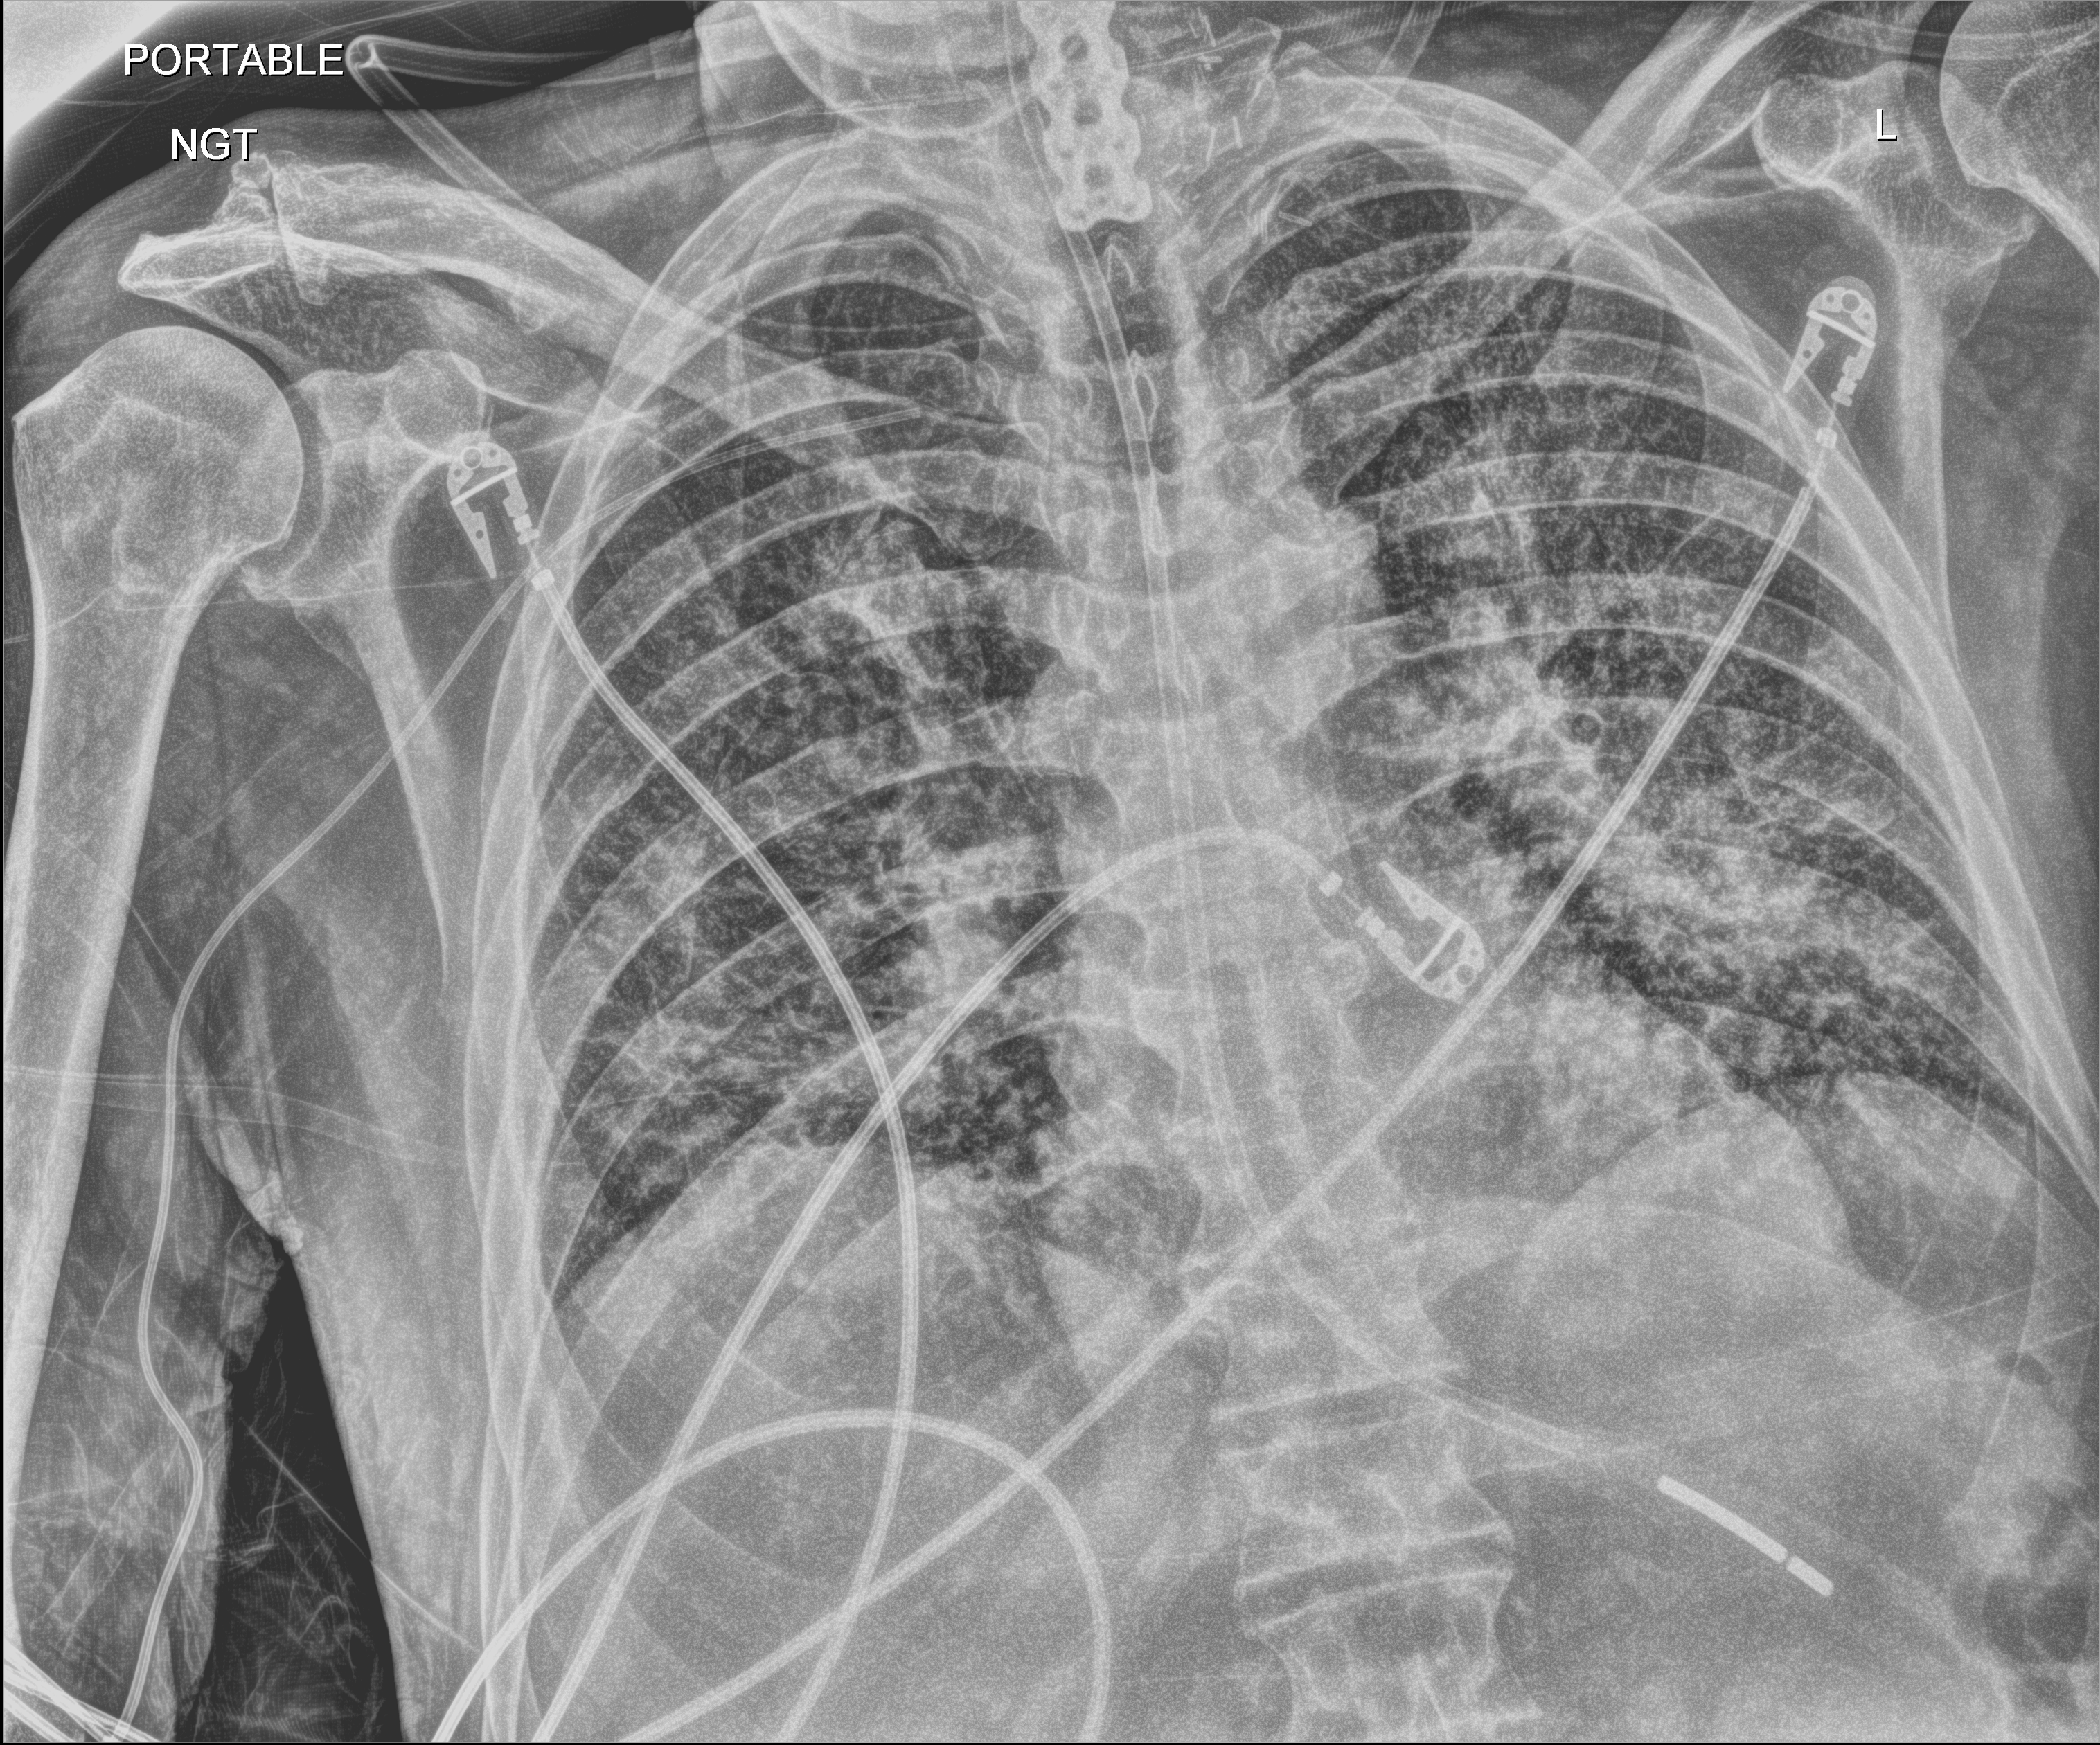
Portable chest radiograph; anteroposterior (AP) projection. Male patient hospitalised with COVID-19, age 60–74 years.
From the hospital-stay record, not from the radiograph (when in the stay this image was taken is not recorded): mechanically ventilated during this hospital stay: yes.